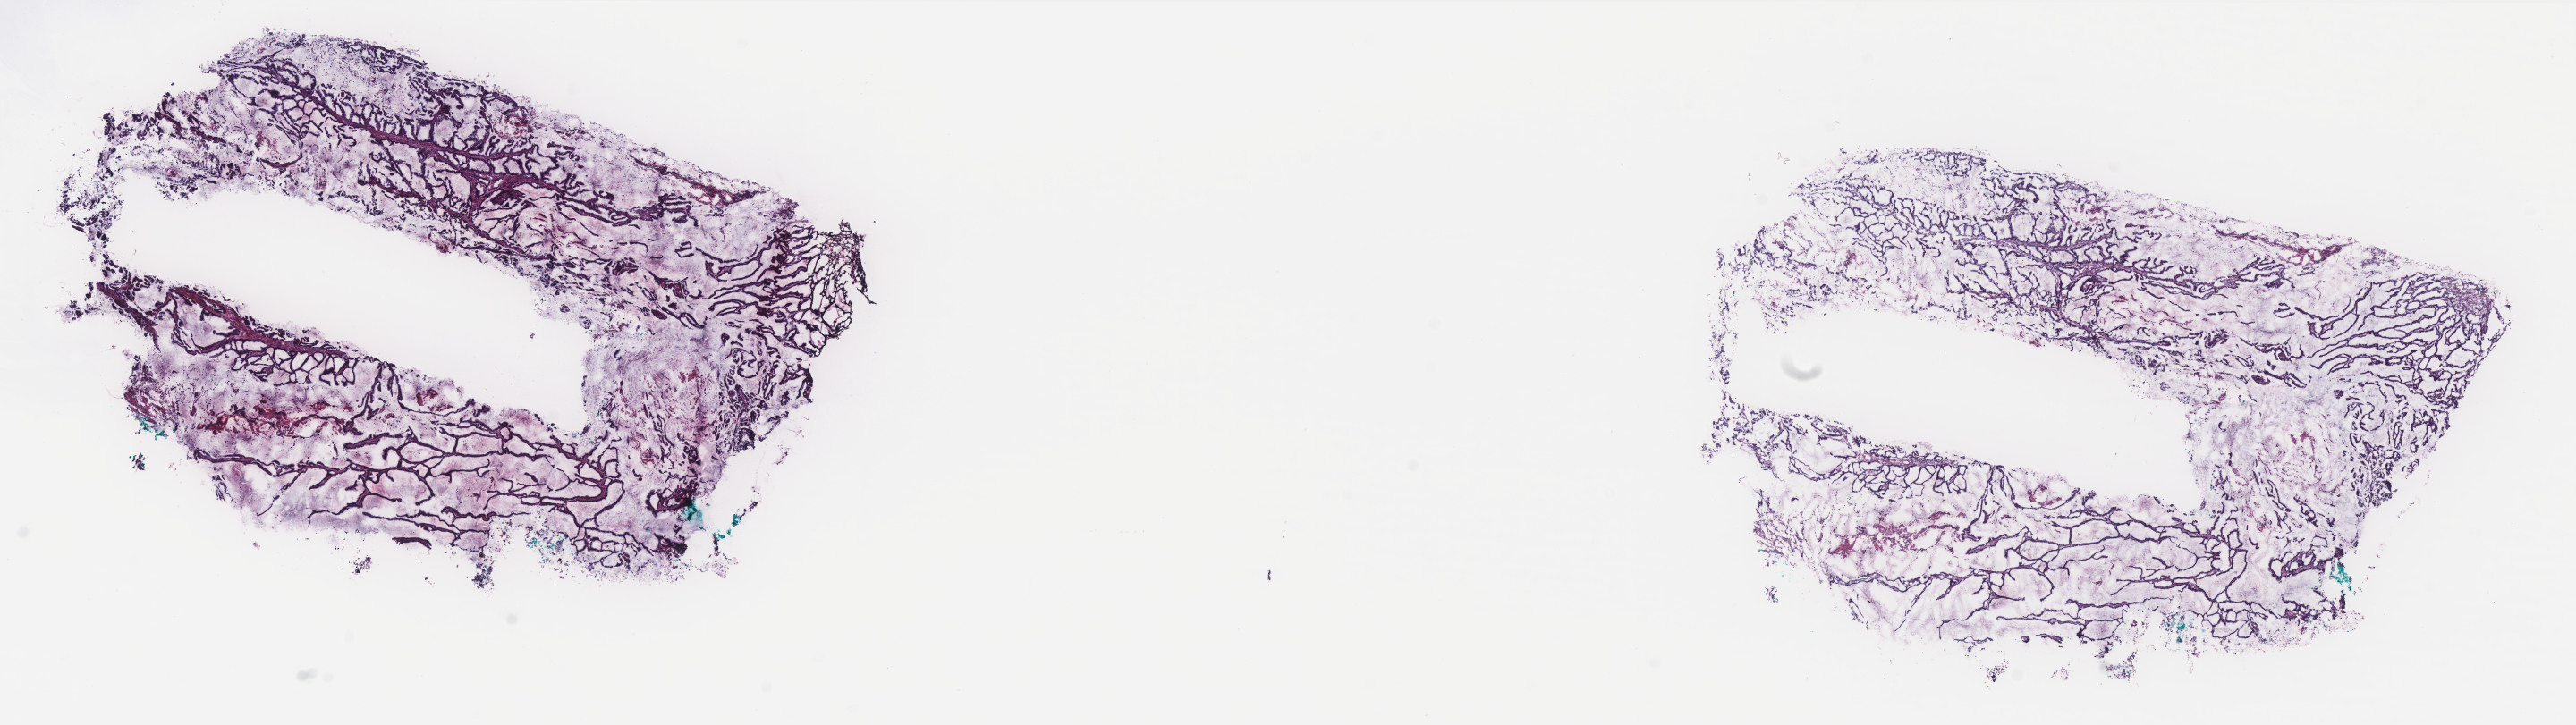
H&E-stained whole-slide image, a low-resolution overview of the entire scanned area, about 23.1 x 6.5 mm. Frozen section from the bottom of the tissue portion. Uterus, primary tumour sample. Patient: female, age at initial diagnosis 56 years. Histologic grade: G1 (well differentiated). Composition of this section per pathologist review: tumour cells 80%, tumour nuclei 80%, normal cells 0%, stromal cells 20%, necrosis 0%. Inflammatory infiltration, as recorded: lymphocyte infiltration 50%, monocyte infiltration 20%, neutrophil infiltration 20%.
Lymph nodes positive (case pathology): 0 of 2 examined. FIGO stage: IB. Histologic diagnosis: Endometrioid adenocarcinoma, NOS.